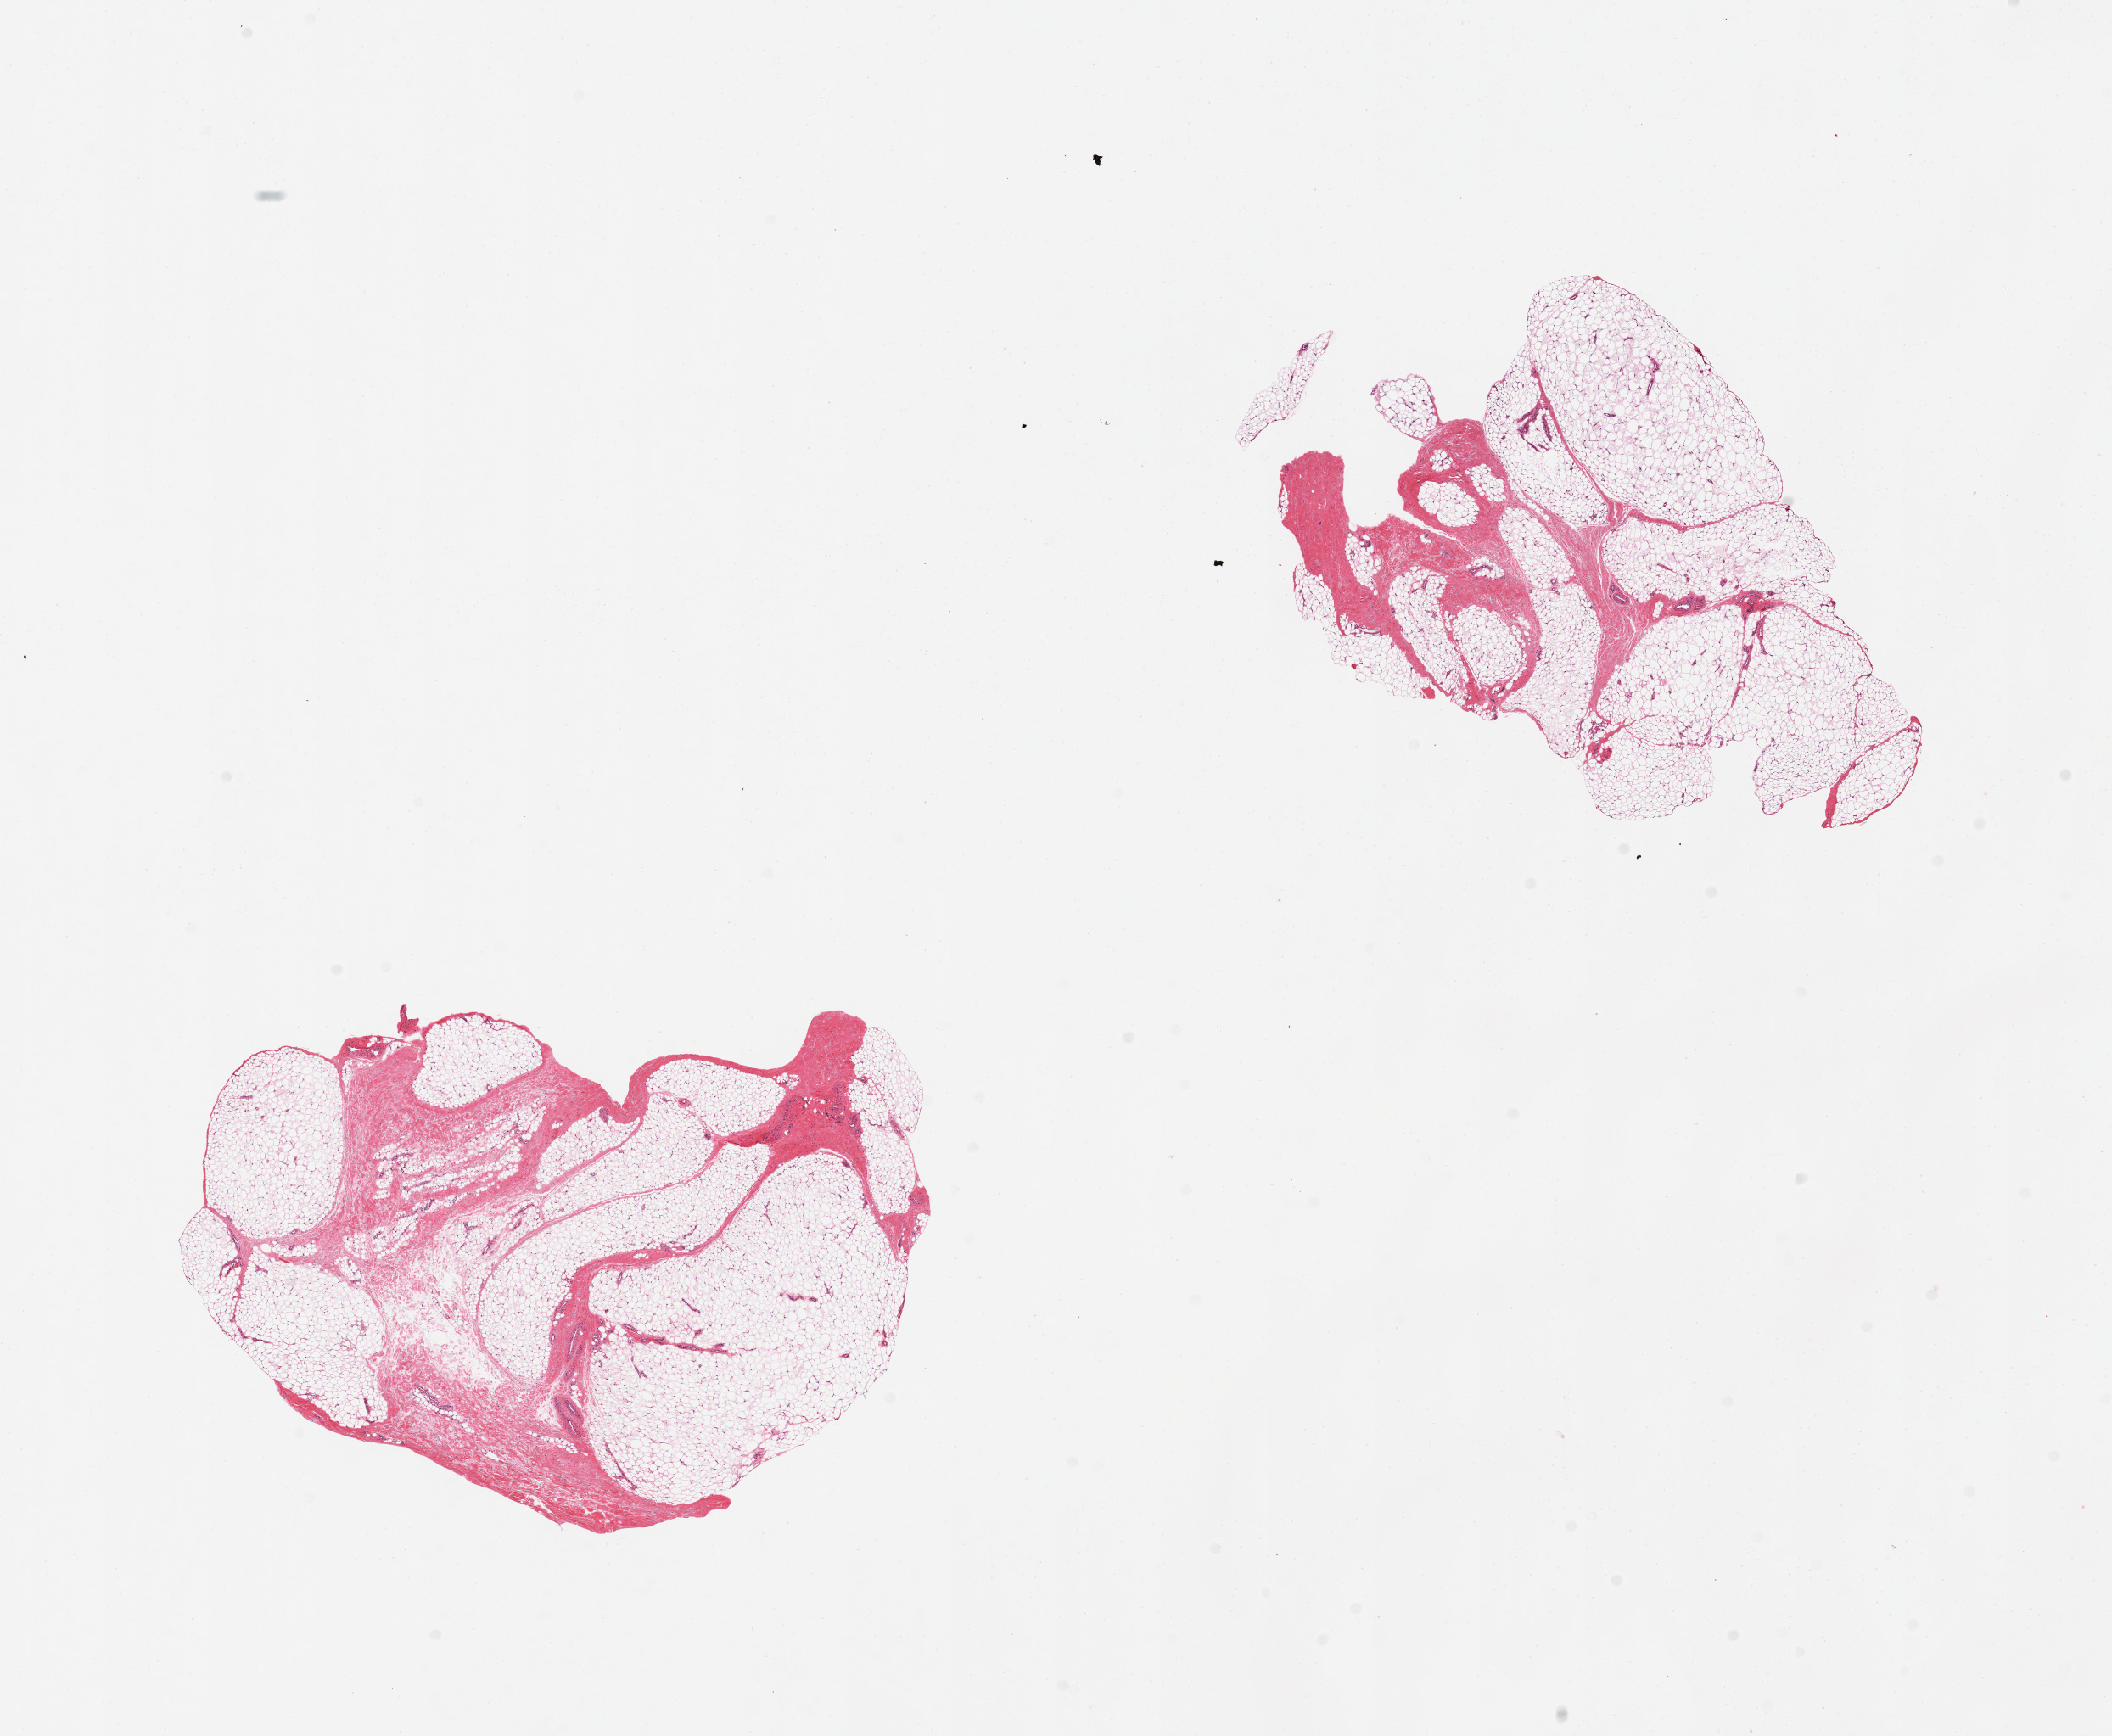
Digitized haematoxylin and eosin-stained section, whole scanned area (about 19.7 x 16.2 mm) shown as a low-resolution overview, PAXgene-fixed paraffin-embedded (PFPE) section, section of adipose tissue (target tissue), donor tissue sample. Donor: male.
Reviewer comment on this tissue sample: 2 pieces; 20% fibrous content.